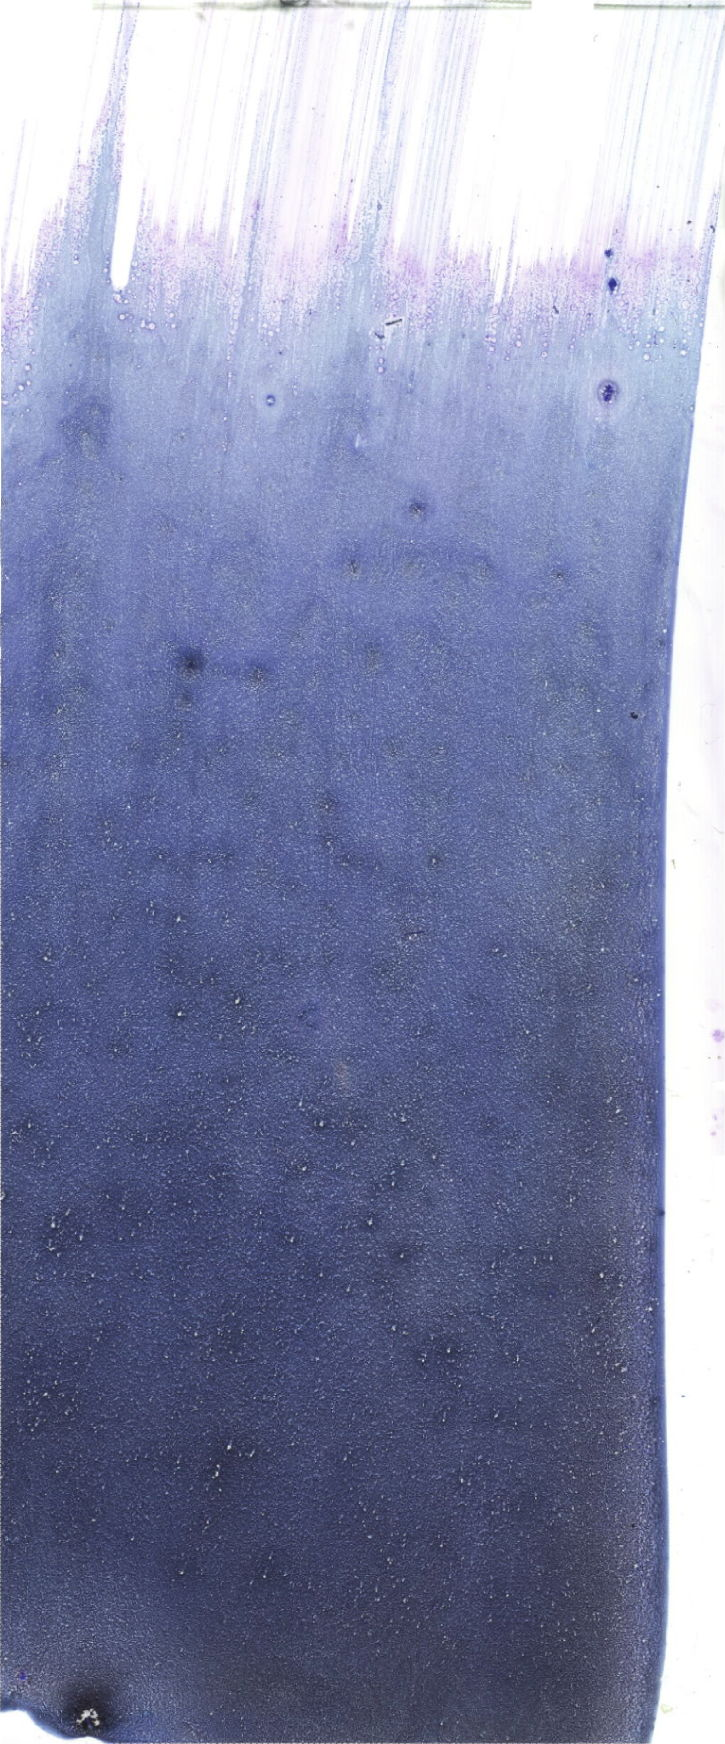
Whole-slide image of a May-Grünwald-Giemsa (MGG)-stained bone marrow aspirate smear — low-resolution overview of the scanned area, about 20.6 x 49.4 mm. Male patient.
Diagnosis: Acute Myelomonocytic Leukemia.